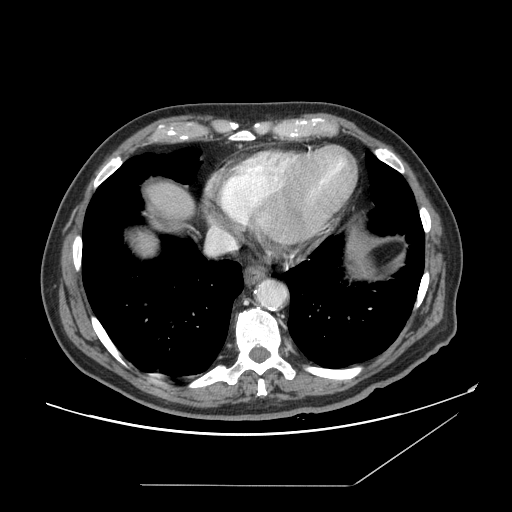
Contrast-enhanced abdominal CT, one axial slice. Position 144 of 166 along the scan axis. 120 kVp. Intravenous contrast given. Soft-tissue window (W 400 / L 40 HU). 2.5 mm slice thickness. 512 × 512 image matrix, field of view 416 × 416 mm. Male patient, age 80 years. Case-level facts recorded for this patient, not image findings: diagnosis: colorectal cancer liver metastases, imaged before liver resection; multiple liver metastases: no; largest metastasis: 2.2 cm; disease in both lobes: no.
Structures marked on this image (manually delineated by an expert):
- liver: box from (x=128, y=183) to (x=195, y=257) px
- planned liver remnant (the part of the liver to remain after resection): (x=129, y=182)–(x=195, y=255)